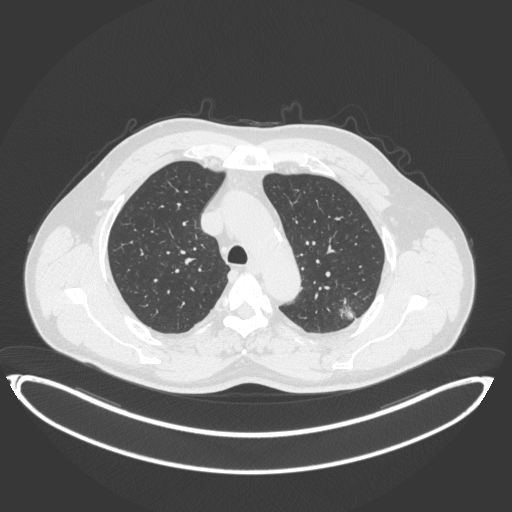
Chest CT, one axial slice. Position 271 of 399 along the scan axis. Reconstruction kernel B31f. 120 kVp. Lung window (W 1500 / L -600 HU). 1 mm slice thickness. 512 × 512 image matrix, field of view 469 × 469 mm. Male patient, age 58 years. From the clinical record (not read from this slice): clinical TNM (as recorded): T1c N0 M0; histopathological grade: G1-2.
Outlined on this slice (bounding box drawn by a radiologist):
- lung tumour (recorded histology: adenocarcinoma): bounding box <339,300,360,324> (left, top, right, bottom; pixels)